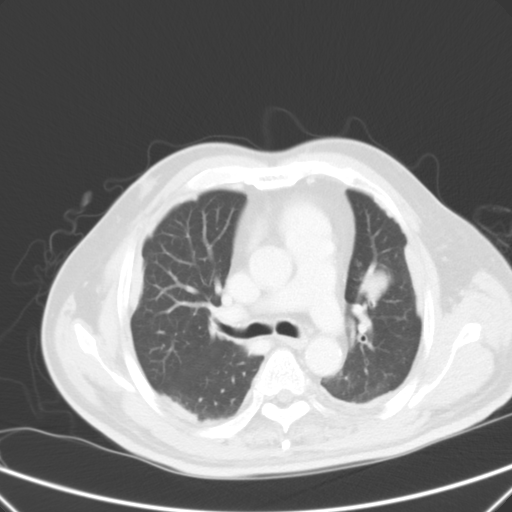
Chest CT, one axial slice; slice 38 of 59 in the series (ordered by position); 120 kVp; intravenous contrast given; lung window (W 1500 / L -600 HU); 5 mm slice thickness; 512 × 512 image matrix, field of view 357 × 357 mm. Male patient, age 66 years. Case-level facts recorded for this patient, not image findings: clinical TNM (as recorded): T1c N3 M1a.
Outlined on this slice (bounding box drawn by a radiologist):
- lung tumour (recorded histology: squamous cell carcinoma): bounding box (x1, y1, x2, y2) in pixels: (355, 261, 395, 307)